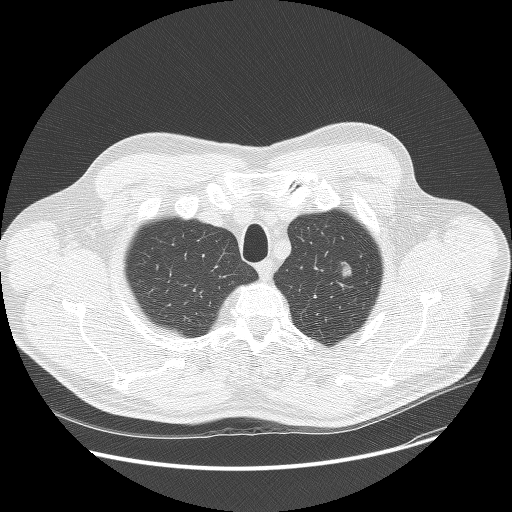
Chest CT (low-dose screening protocol), one axial image; baseline annual screen; lung window (W 1500 / L -600 HU); 2.5 mm slice thickness; 120 kVp. Male, age 60 years at enrolment. Former smoker at enrolment.
Expert-annotated lung lesion, bounding box [x1, y1, x2, y2] px = [329, 248, 370, 293]. The screening reader recorded 2 non-calcified nodules or masses ≥4 mm on this exam (left upper lobe, right lower lobe); which of them this box marks is not recorded. Official screen result: positive, change unspecified: nodule(s) >= 4 mm or enlarging nodule(s), mass(es), or other non-specific abnormalities suspicious for lung cancer.